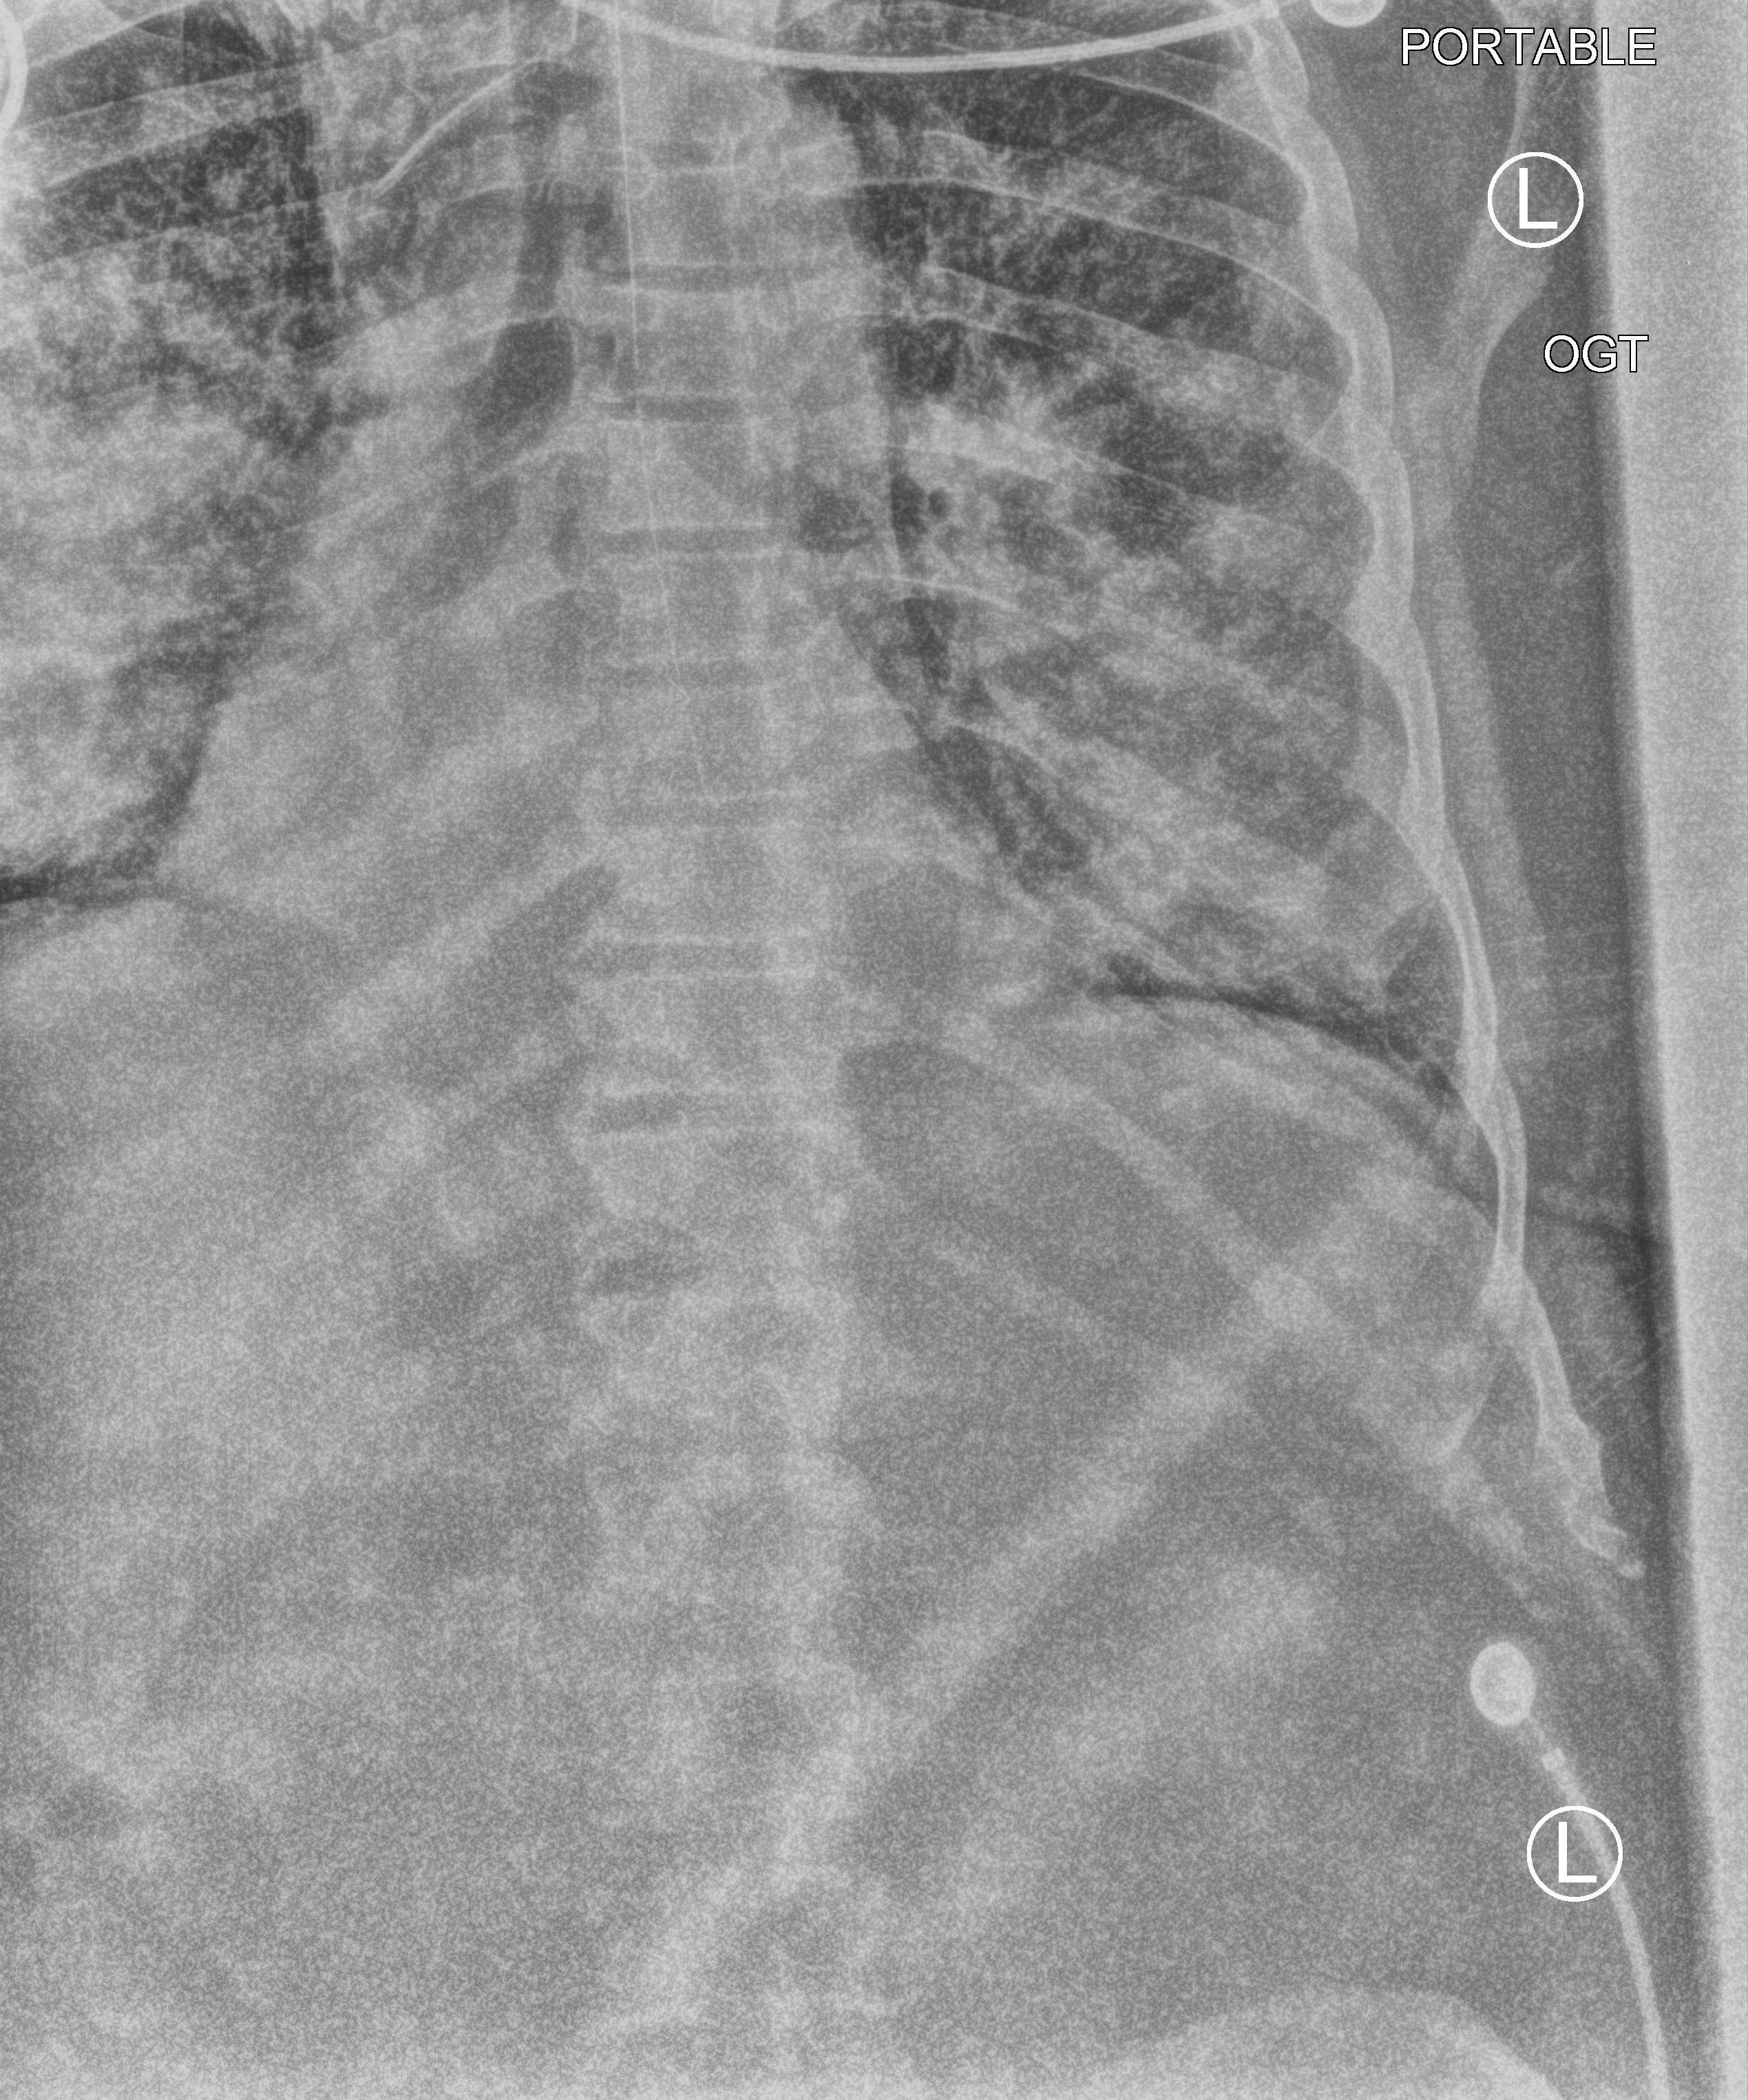
Bedside chest radiograph (computed radiography); anteroposterior (AP) projection. Adult patient hospitalised with COVID-19, age 18–59 years.
From the hospital-stay record, not from the radiograph (when in the stay this image was taken is not recorded):
- admitted to intensive care during this hospital stay: yes
- smoking status (admission record): never
- mechanically ventilated during this hospital stay: yes